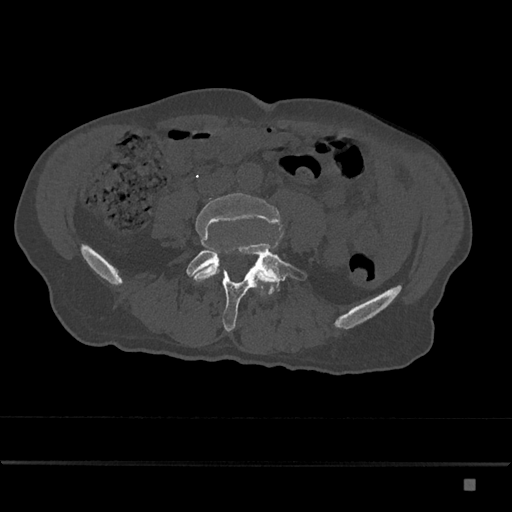
CT including the spine, one axial slice; position 301 of 797 along the scan axis; reconstruction kernel Br40s/3; 120 kVp; bone window (W 1800 / L 400 HU); 0.5 mm slice thickness; 512 × 512 image matrix, field of view 390 × 390 mm. Patient: male, 72 years. Case-level facts recorded for this patient, not image findings: primary cancer: prostate.
Structures marked on this image (semi-automatically segmented with operator editing):
- L4 vertebra: bounding box (x1, y1, x2, y2) in pixels: (190, 193, 282, 282)
- L5 vertebra: (186, 243, 307, 332)